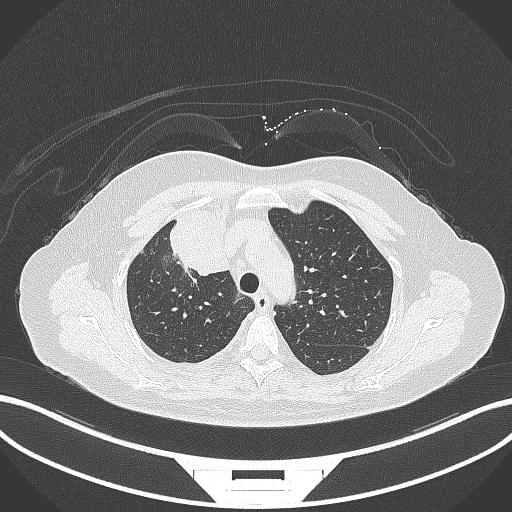
Chest CT, one axial slice. Slice 227 of 305 in the series (ordered by position). 120 kVp. Lung window (W 1500 / L -600 HU). 1 mm slice thickness. 512 × 512 image matrix. Patient: female, 52 years. From the clinical record (not read from this slice): clinical TNM (as recorded): T3 N1 M1.
Structures marked on this image (bounding box drawn by a radiologist):
- lung tumour (recorded histology: adenocarcinoma): box from (x=161, y=209) to (x=231, y=278) px